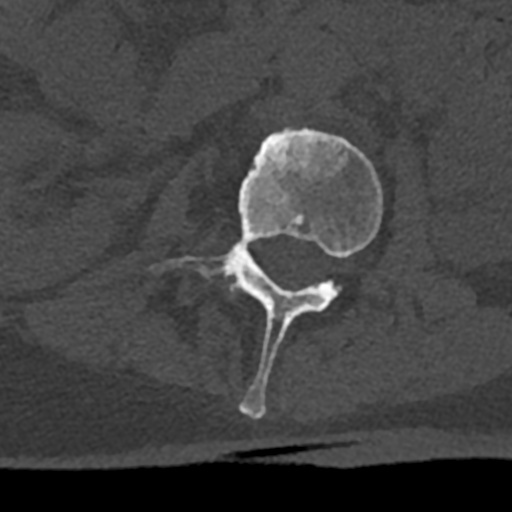
CT including the spine, one axial slice. Reconstruction kernel Br40s/3. 120 kVp. Bone window (W 1800 / L 400 HU). 0.5 mm slice thickness. 512 × 512 image matrix. Male patient, age 74 years. Case-level facts recorded for this patient, not image findings: primary cancer: renal.
Structures marked on this image (semi-automatically segmented with operator editing):
- L2 vertebra: bounding box (x1, y1, x2, y2) in pixels: (152, 127, 382, 419)
- L3 vertebra: (231, 282, 244, 291)